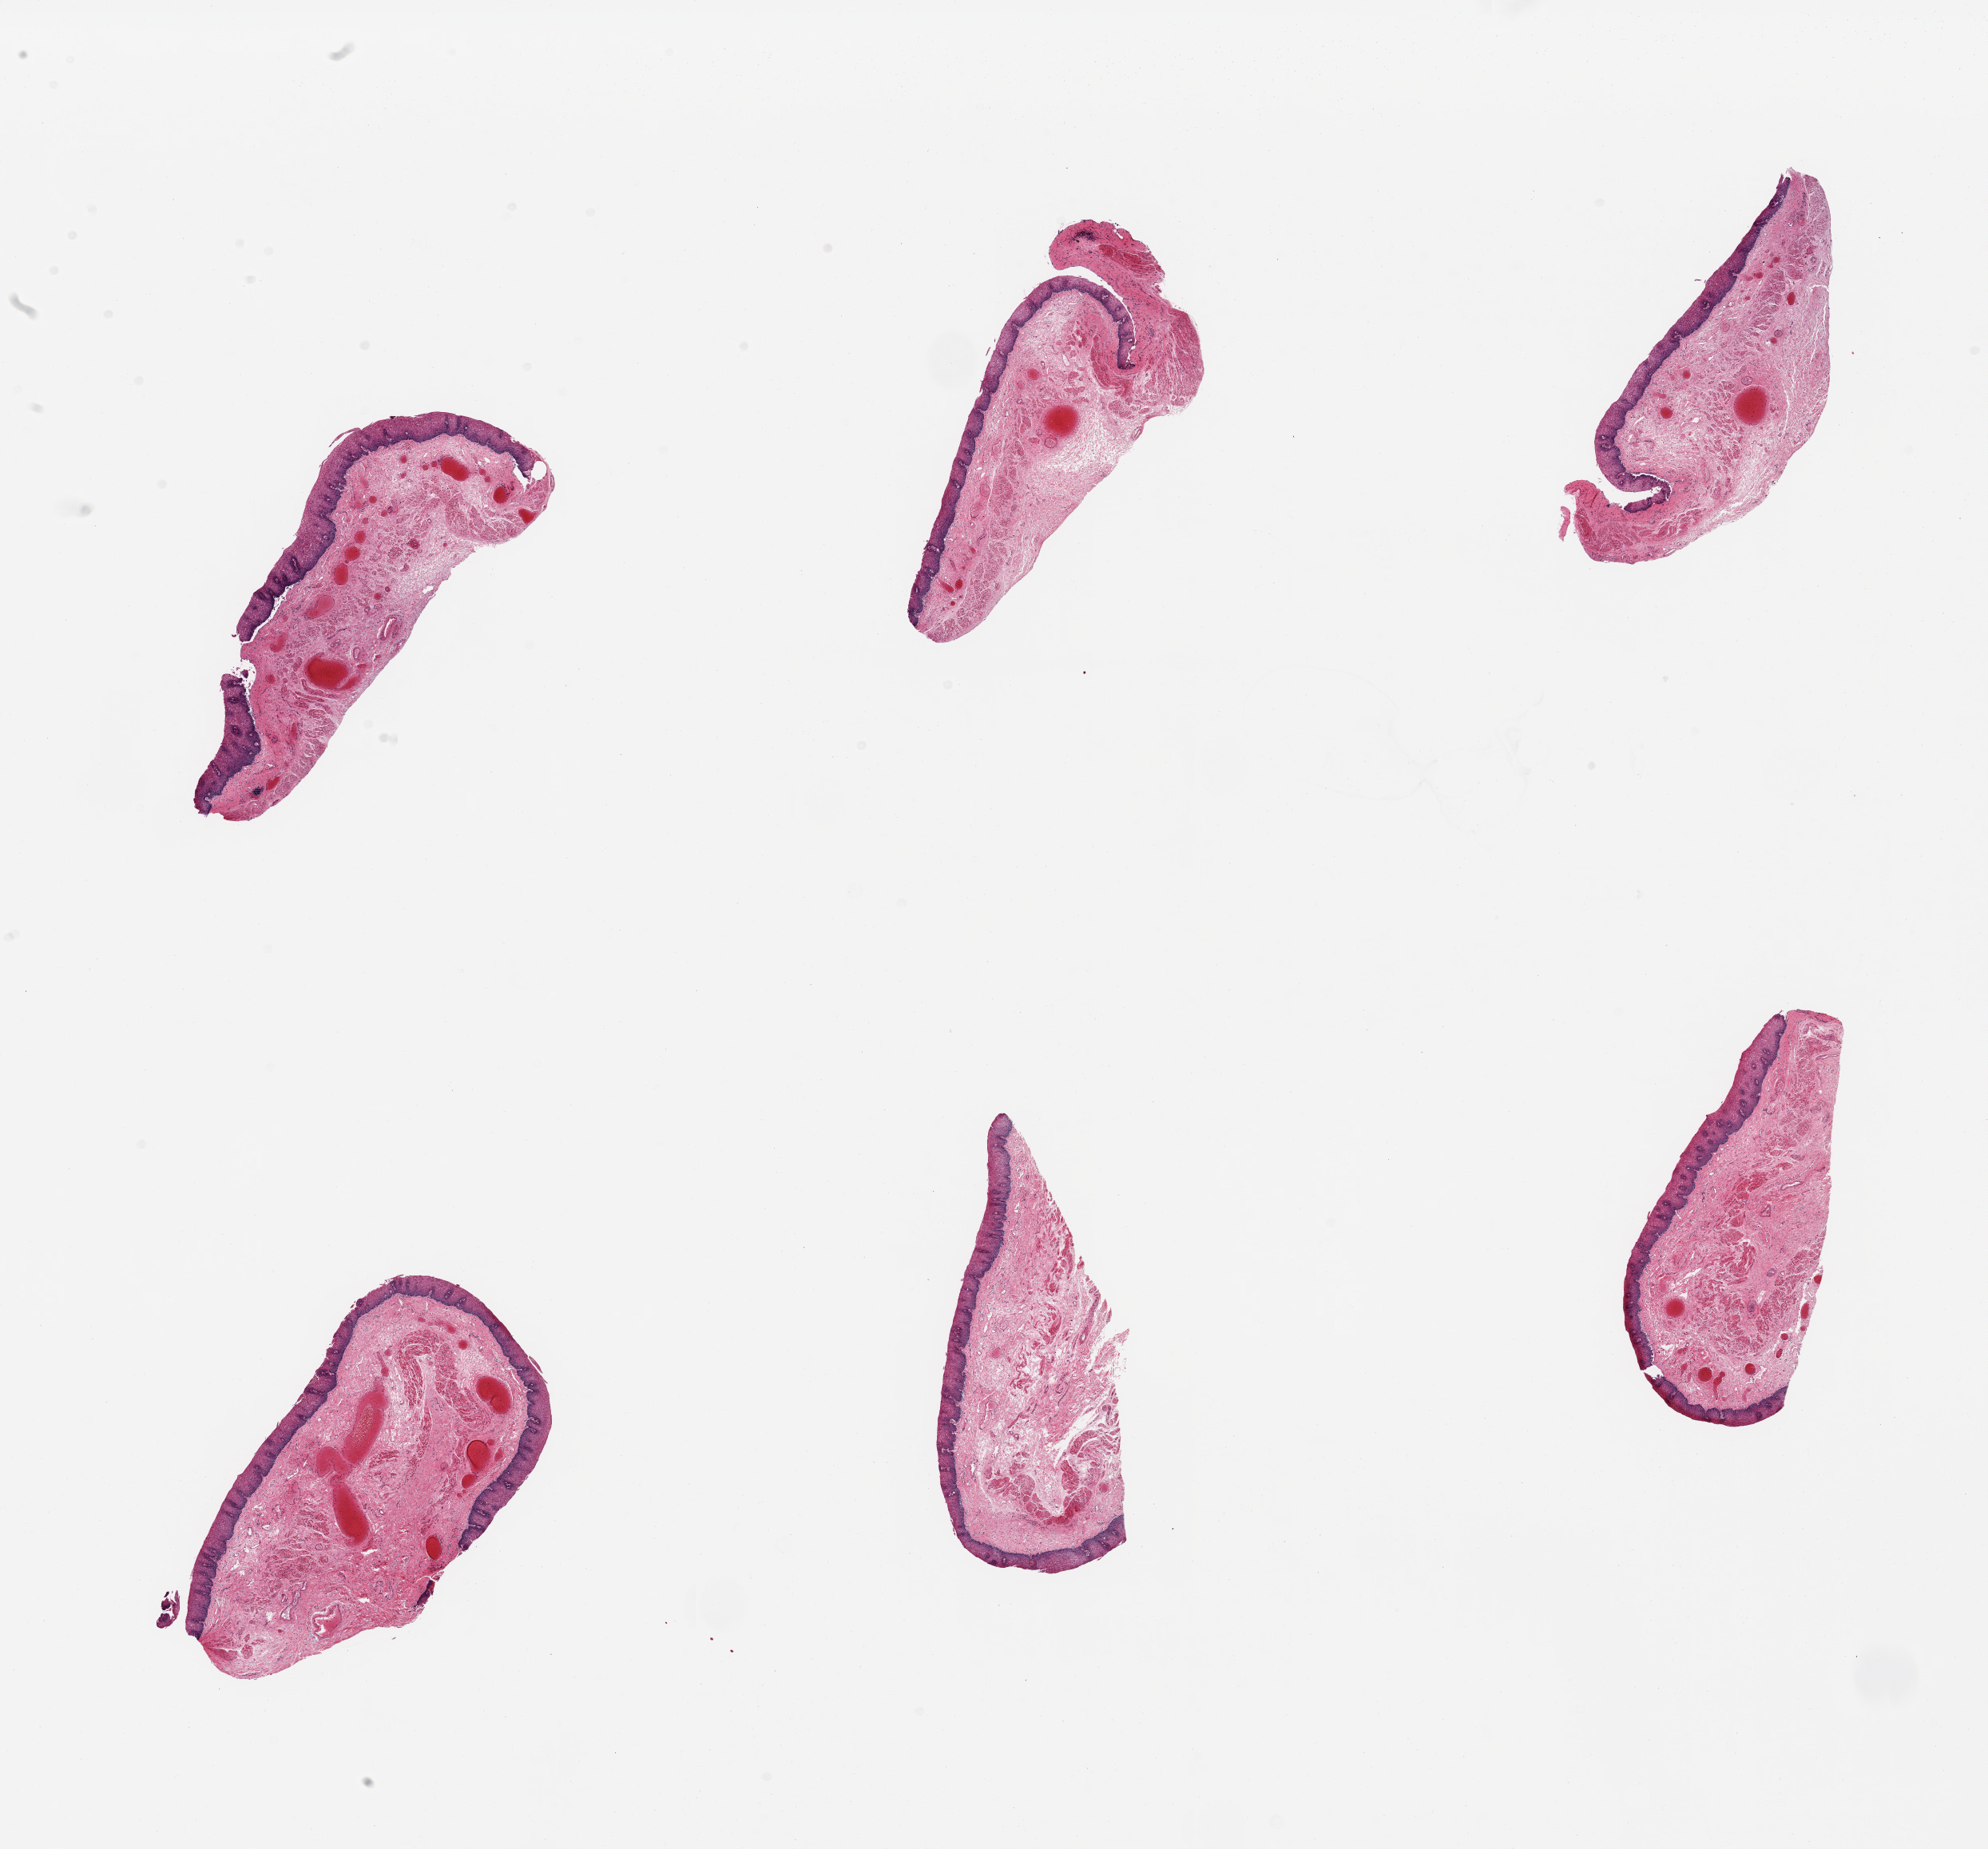
Haematoxylin and eosin whole-slide image — whole scanned area (about 19.7 x 18.3 mm) shown as a low-resolution overview, PAXgene-fixed, paraffin-embedded tissue, section of esophageal mucous membrane (target tissue), tissue donor sample. Donor: male.
Review note (as recorded): 6 pieces, squamous mucosa is ~0.3mm, ~20% thickness.